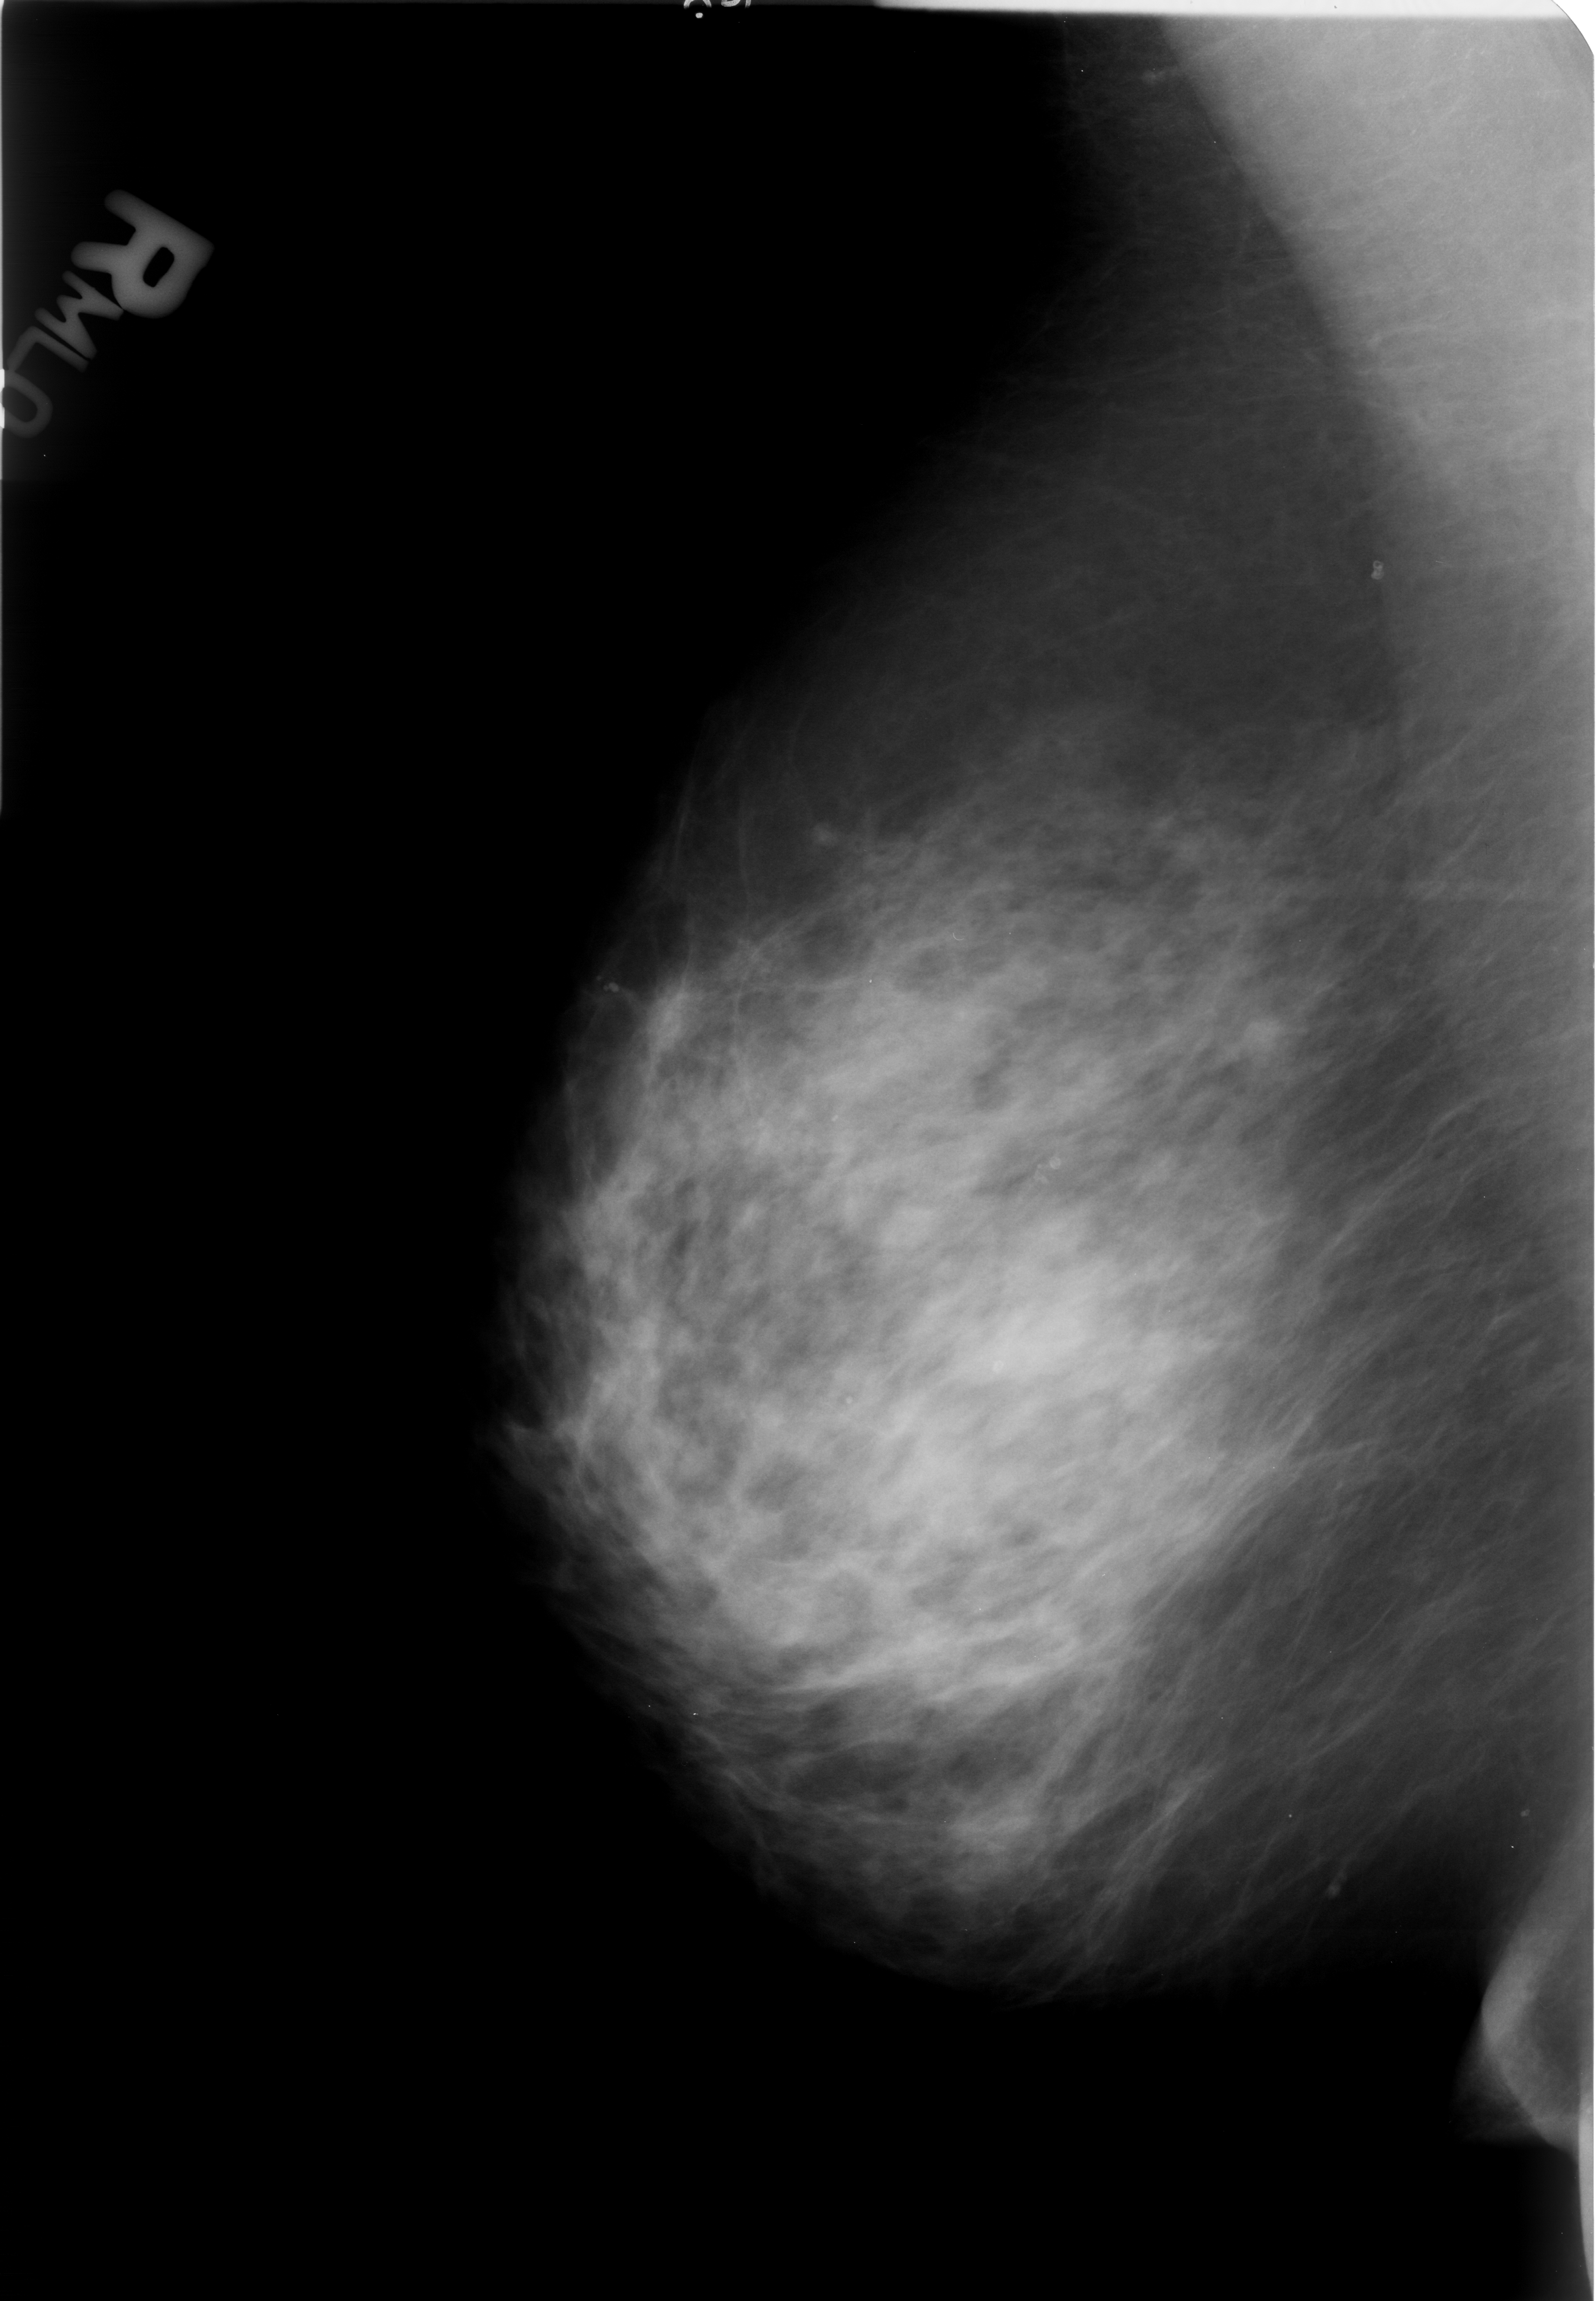
Digitized screen-film mammogram; right breast; MLO view; breast composition: heterogeneously dense (BI-RADS density category 3 of 4).
Radiologist-marked abnormalities on this image: Finding 1 of 3: calcifications, morphology lucent centered; BI-RADS assessment category 2; subtlety rating 3 on a 1 (subtle) to 5 (obvious) scale; benign; no additional work-up was recommended (benign without callback). Finding 2 of 3: calcifications, morphology lucent centered; BI-RADS assessment category 2; subtlety rating 3 on a 1 (subtle) to 5 (obvious) scale; benign; no additional work-up was recommended (benign without callback). Finding 3 of 3: calcifications, morphology lucent centered; BI-RADS assessment category 2; subtlety rating 3 on a 1 (subtle) to 5 (obvious) scale; benign; no additional work-up was recommended (benign without callback).